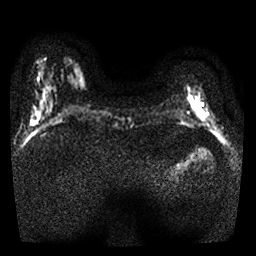
Breast MRI, one axial slice. Diffusion-weighted series; image 2 of 4 stored at this slice position (different b-values; order by instance number). 1.5 T. 256 × 256 image matrix, field of view 300 × 300 mm. Female patient.
Annotated regions visible in this slice (outlined manually by an expert reader):
- tumour on diffusion-weighted imaging: bounding box <188,95,206,122> (left, top, right, bottom; pixels)